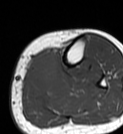
MRI of an extremity soft-tissue mass, one axial slice; position 20 of 68 along the scan axis; MR volume resampled by the dataset authors to the PET/CT grid (not the native acquisition matrix); 3.27 mm slice thickness; 123 × 134 image matrix. Female patient. Case-level facts recorded for this patient, not image findings: histological type: extraskeletal high grade osteogenic sarcoma; grade: high; site of the primary tumour: left calf.
Outlined on this slice (expert contour drawn on MRI and transferred to this co-registered scan by the dataset authors):
- gross tumour volume (mass): bounding box (x1, y1, x2, y2) in pixels: (26, 50, 59, 95)